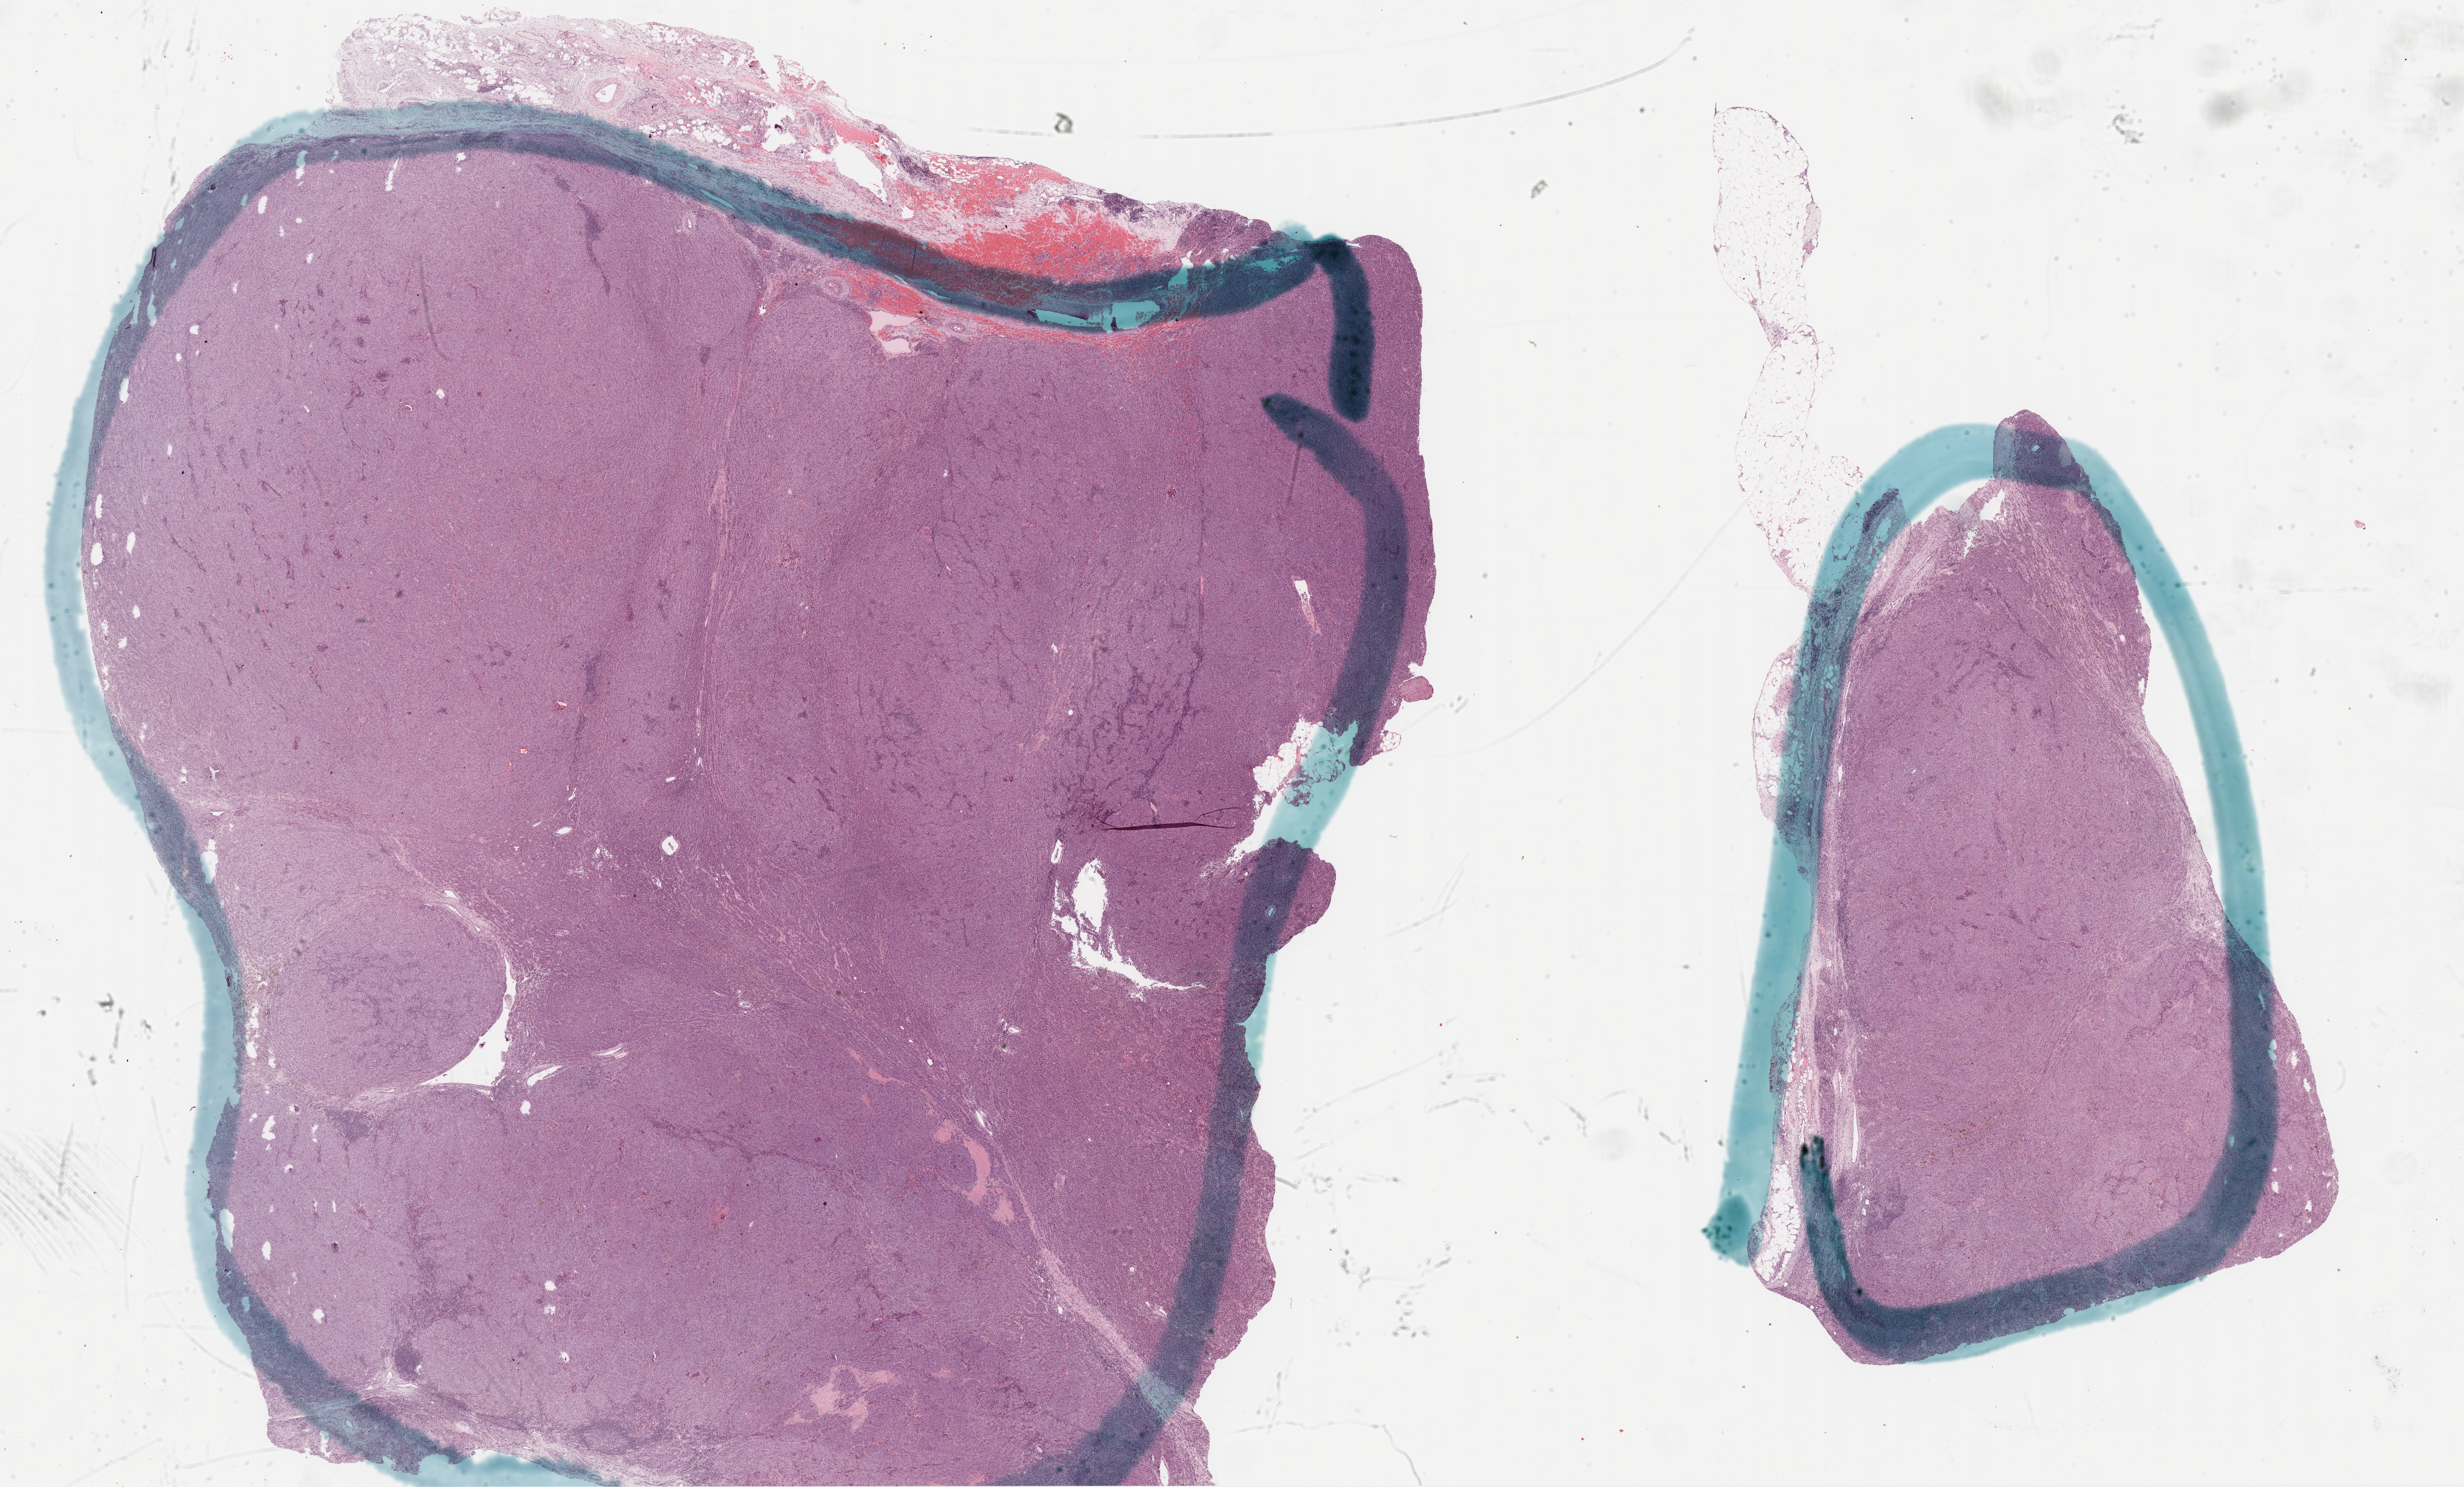
Digitized H&E tissue section (whole slide) — a low-resolution overview of the entire scanned area, about 32.7 x 19.7 mm; formalin-fixed paraffin-embedded (FFPE) diagnostic section; metastatic tumour sample, sampled site not recorded. Male patient; age at initial diagnosis 55 years.
This section: metastatic tumour tissue. Patient diagnosis: Malignant melanoma, NOS.